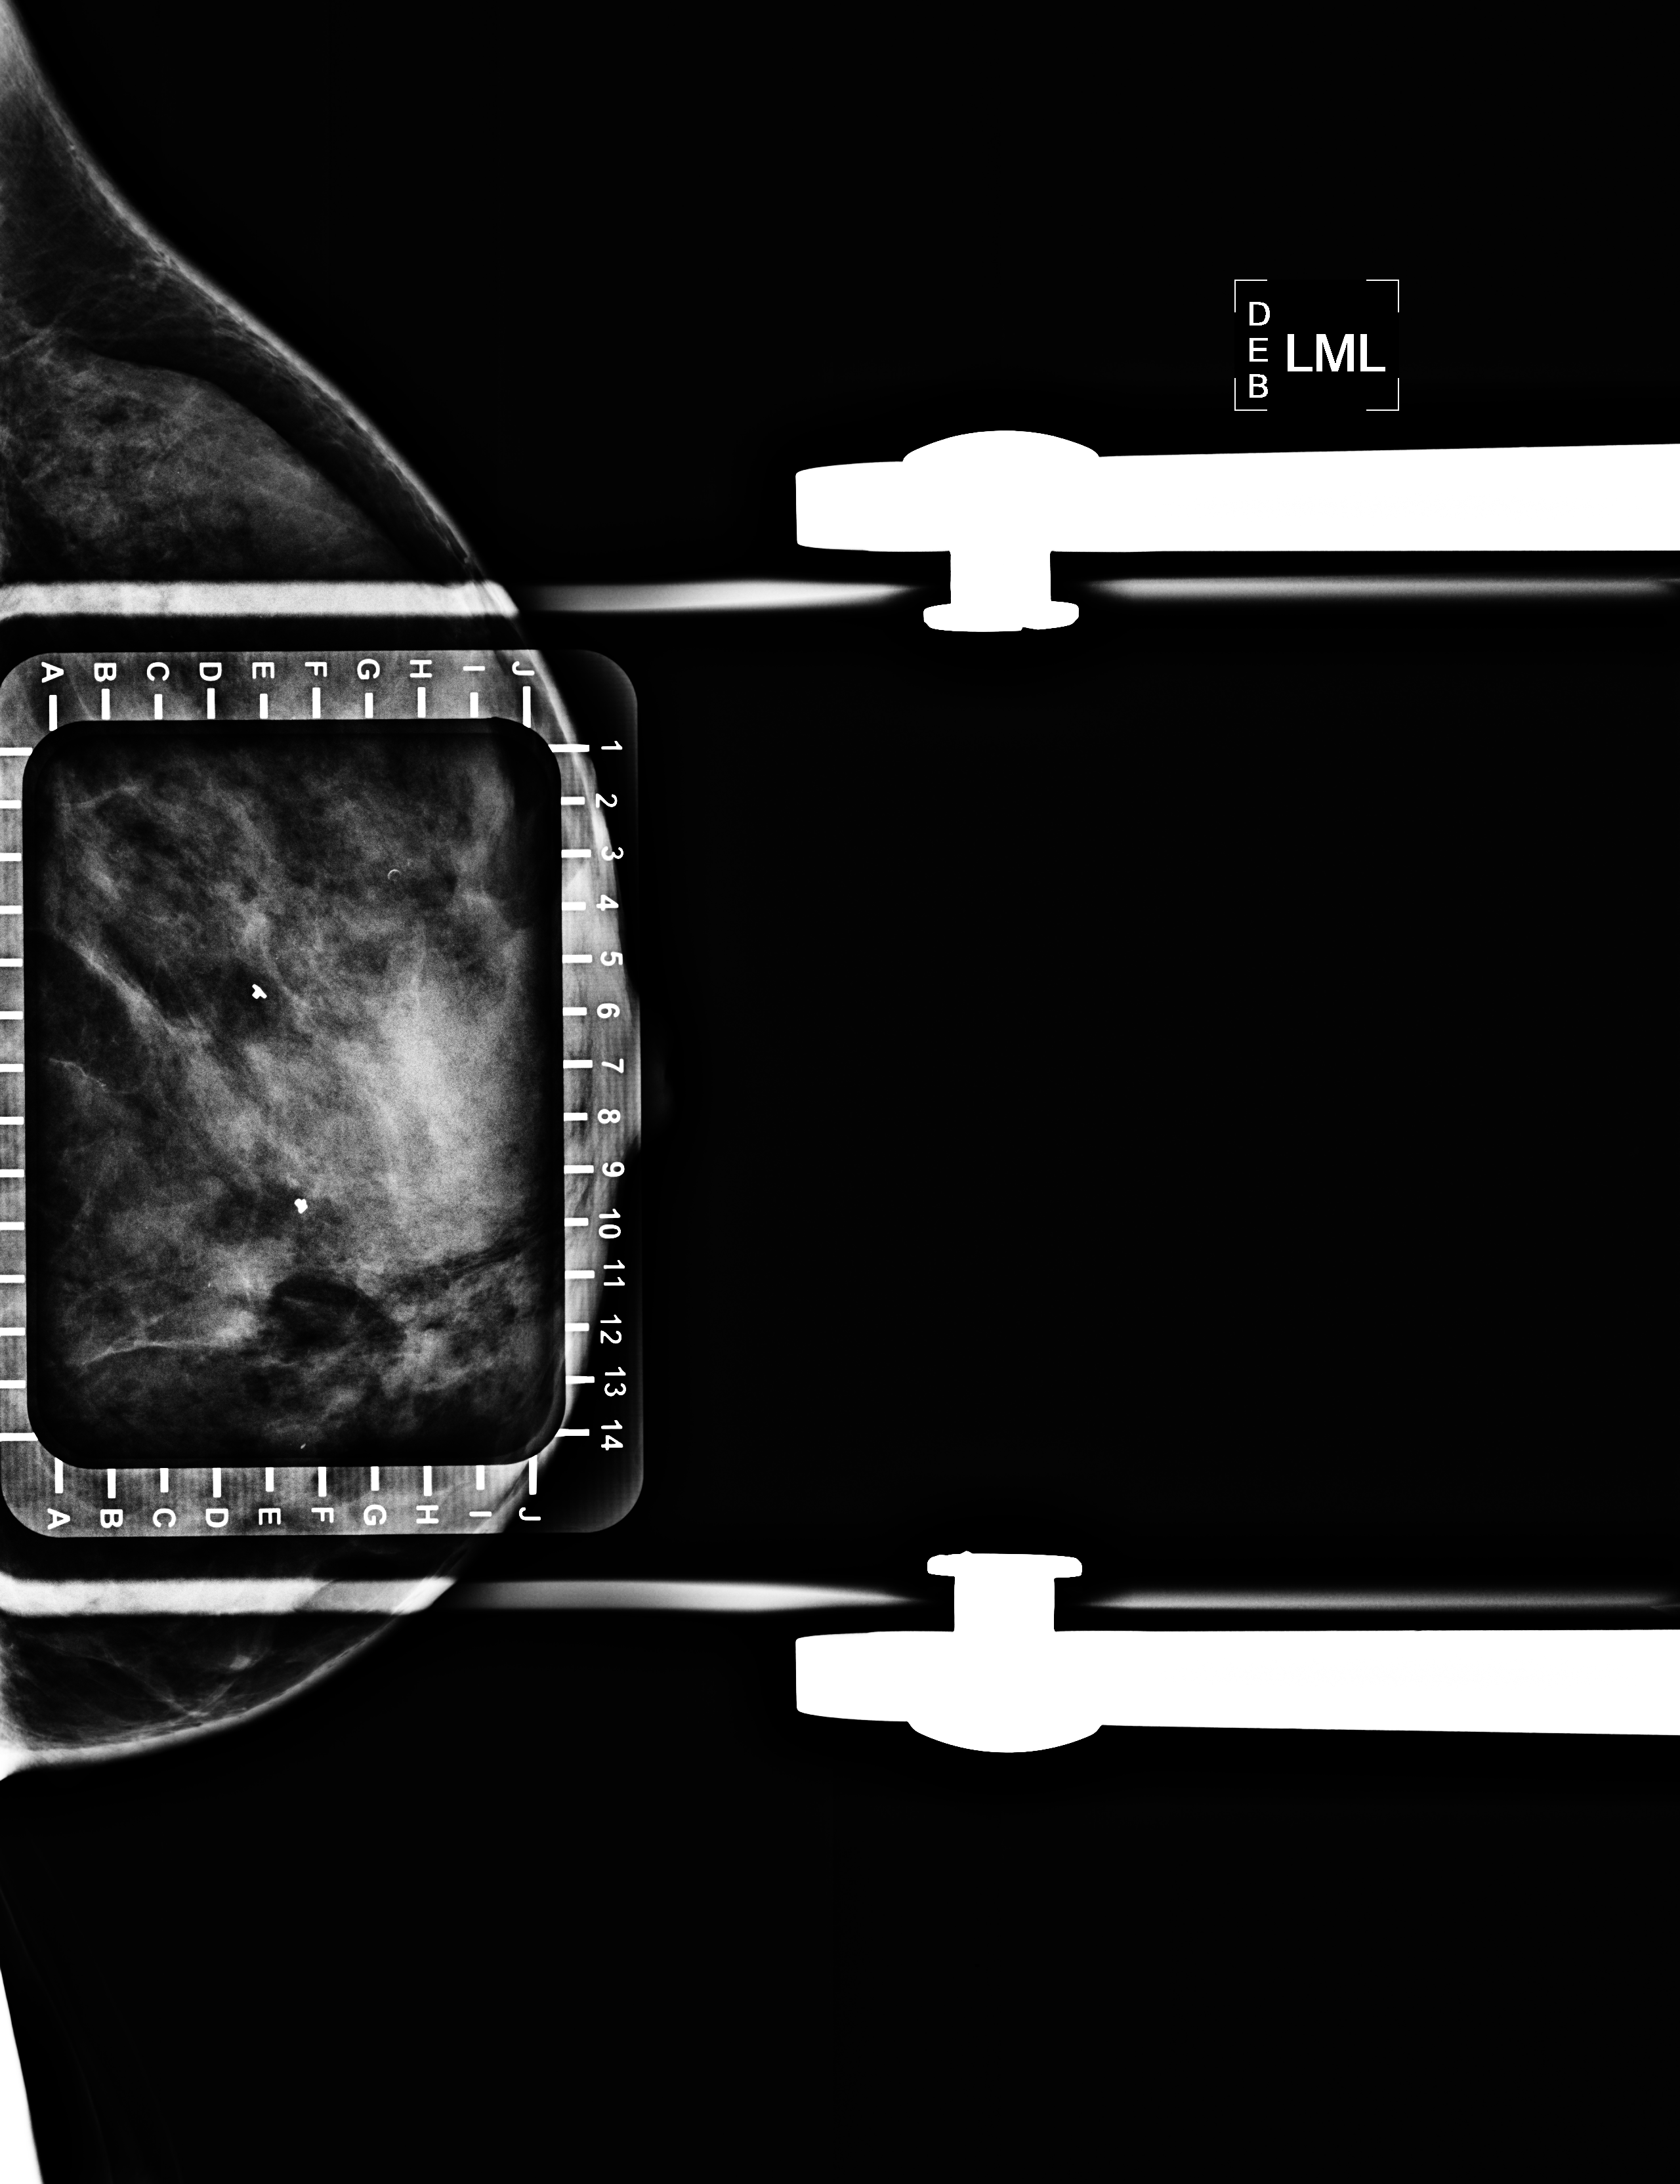
Needle-localisation mammographic view, left breast, ML view.
Pathology recorded for this patient (not read from this image): pathology diagnosis: ducta CA in situ (left breast); receptor status (as recorded): ER neg, PR neg, HER2 pos.